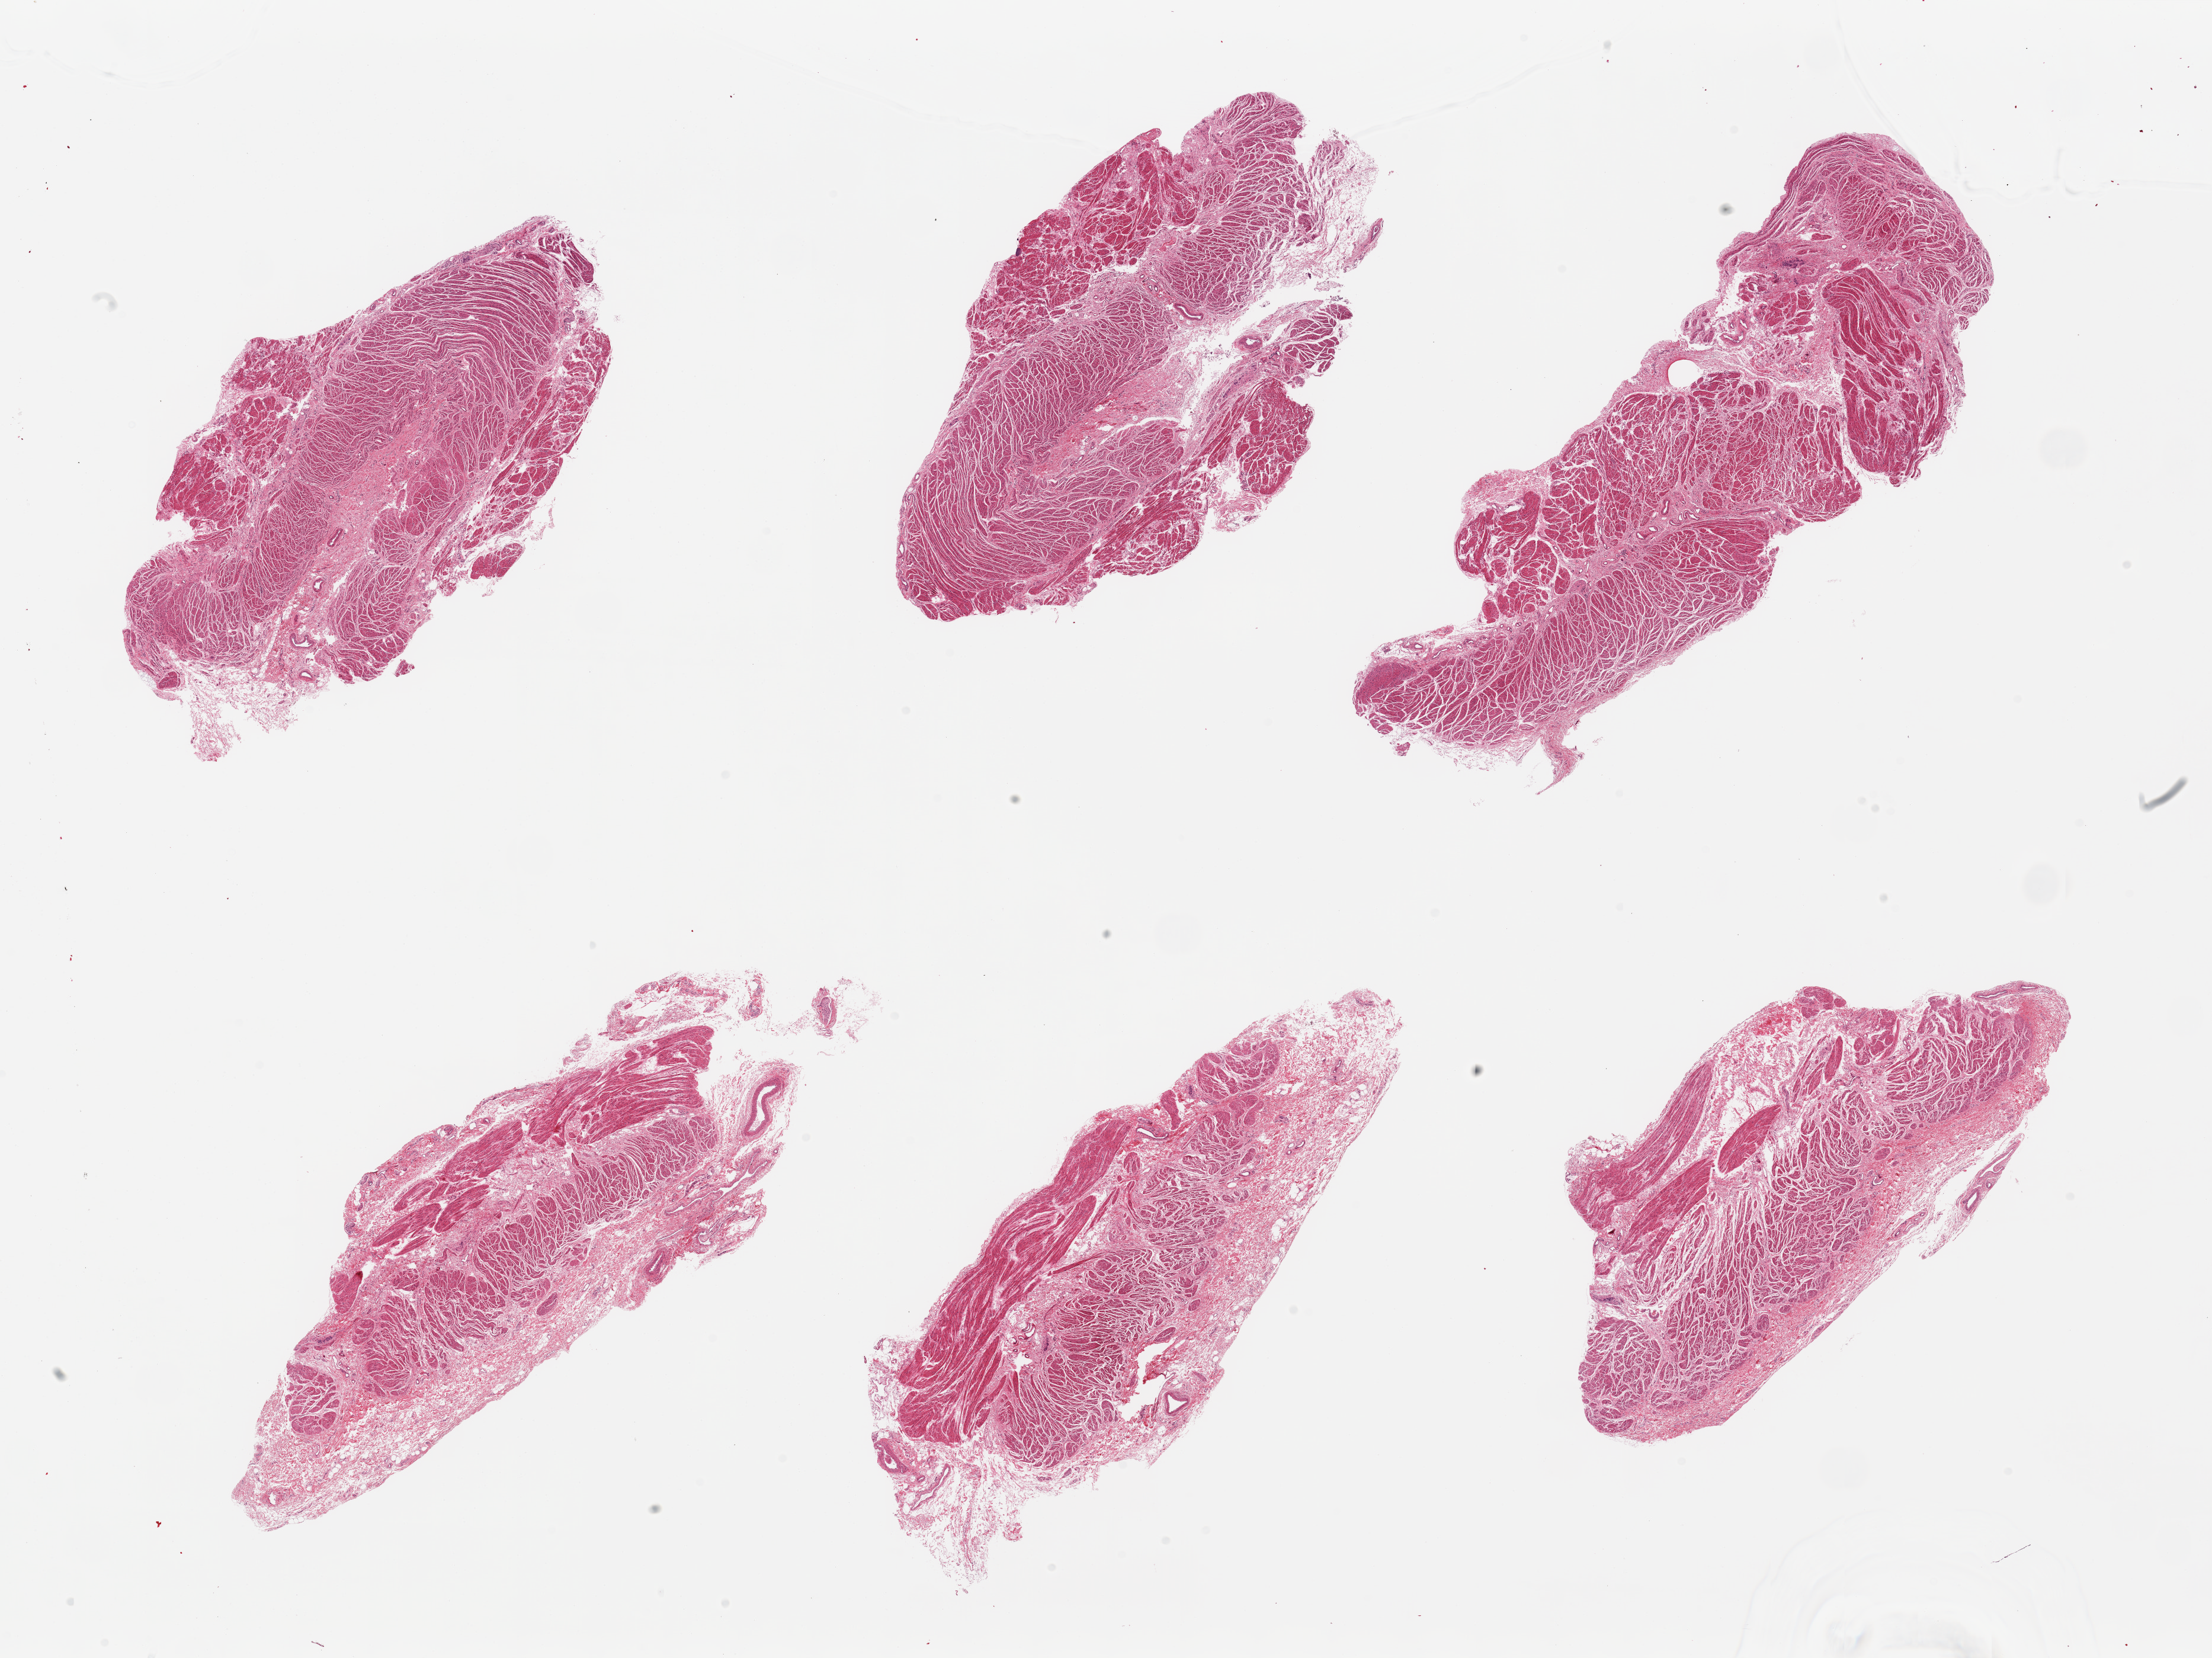
Whole-slide image, H&E stain — a low-resolution overview of the entire scanned area, about 29.5 x 22.1 mm (acquisition: 20x scan); PAXgene-fixed paraffin-embedded (PFPE) section; section of gastroesophageal junction (target tissue); donor tissue sample. Donor: female.
• pathologist's review note for this sample: 6 pieces, all muscularis, good specimens